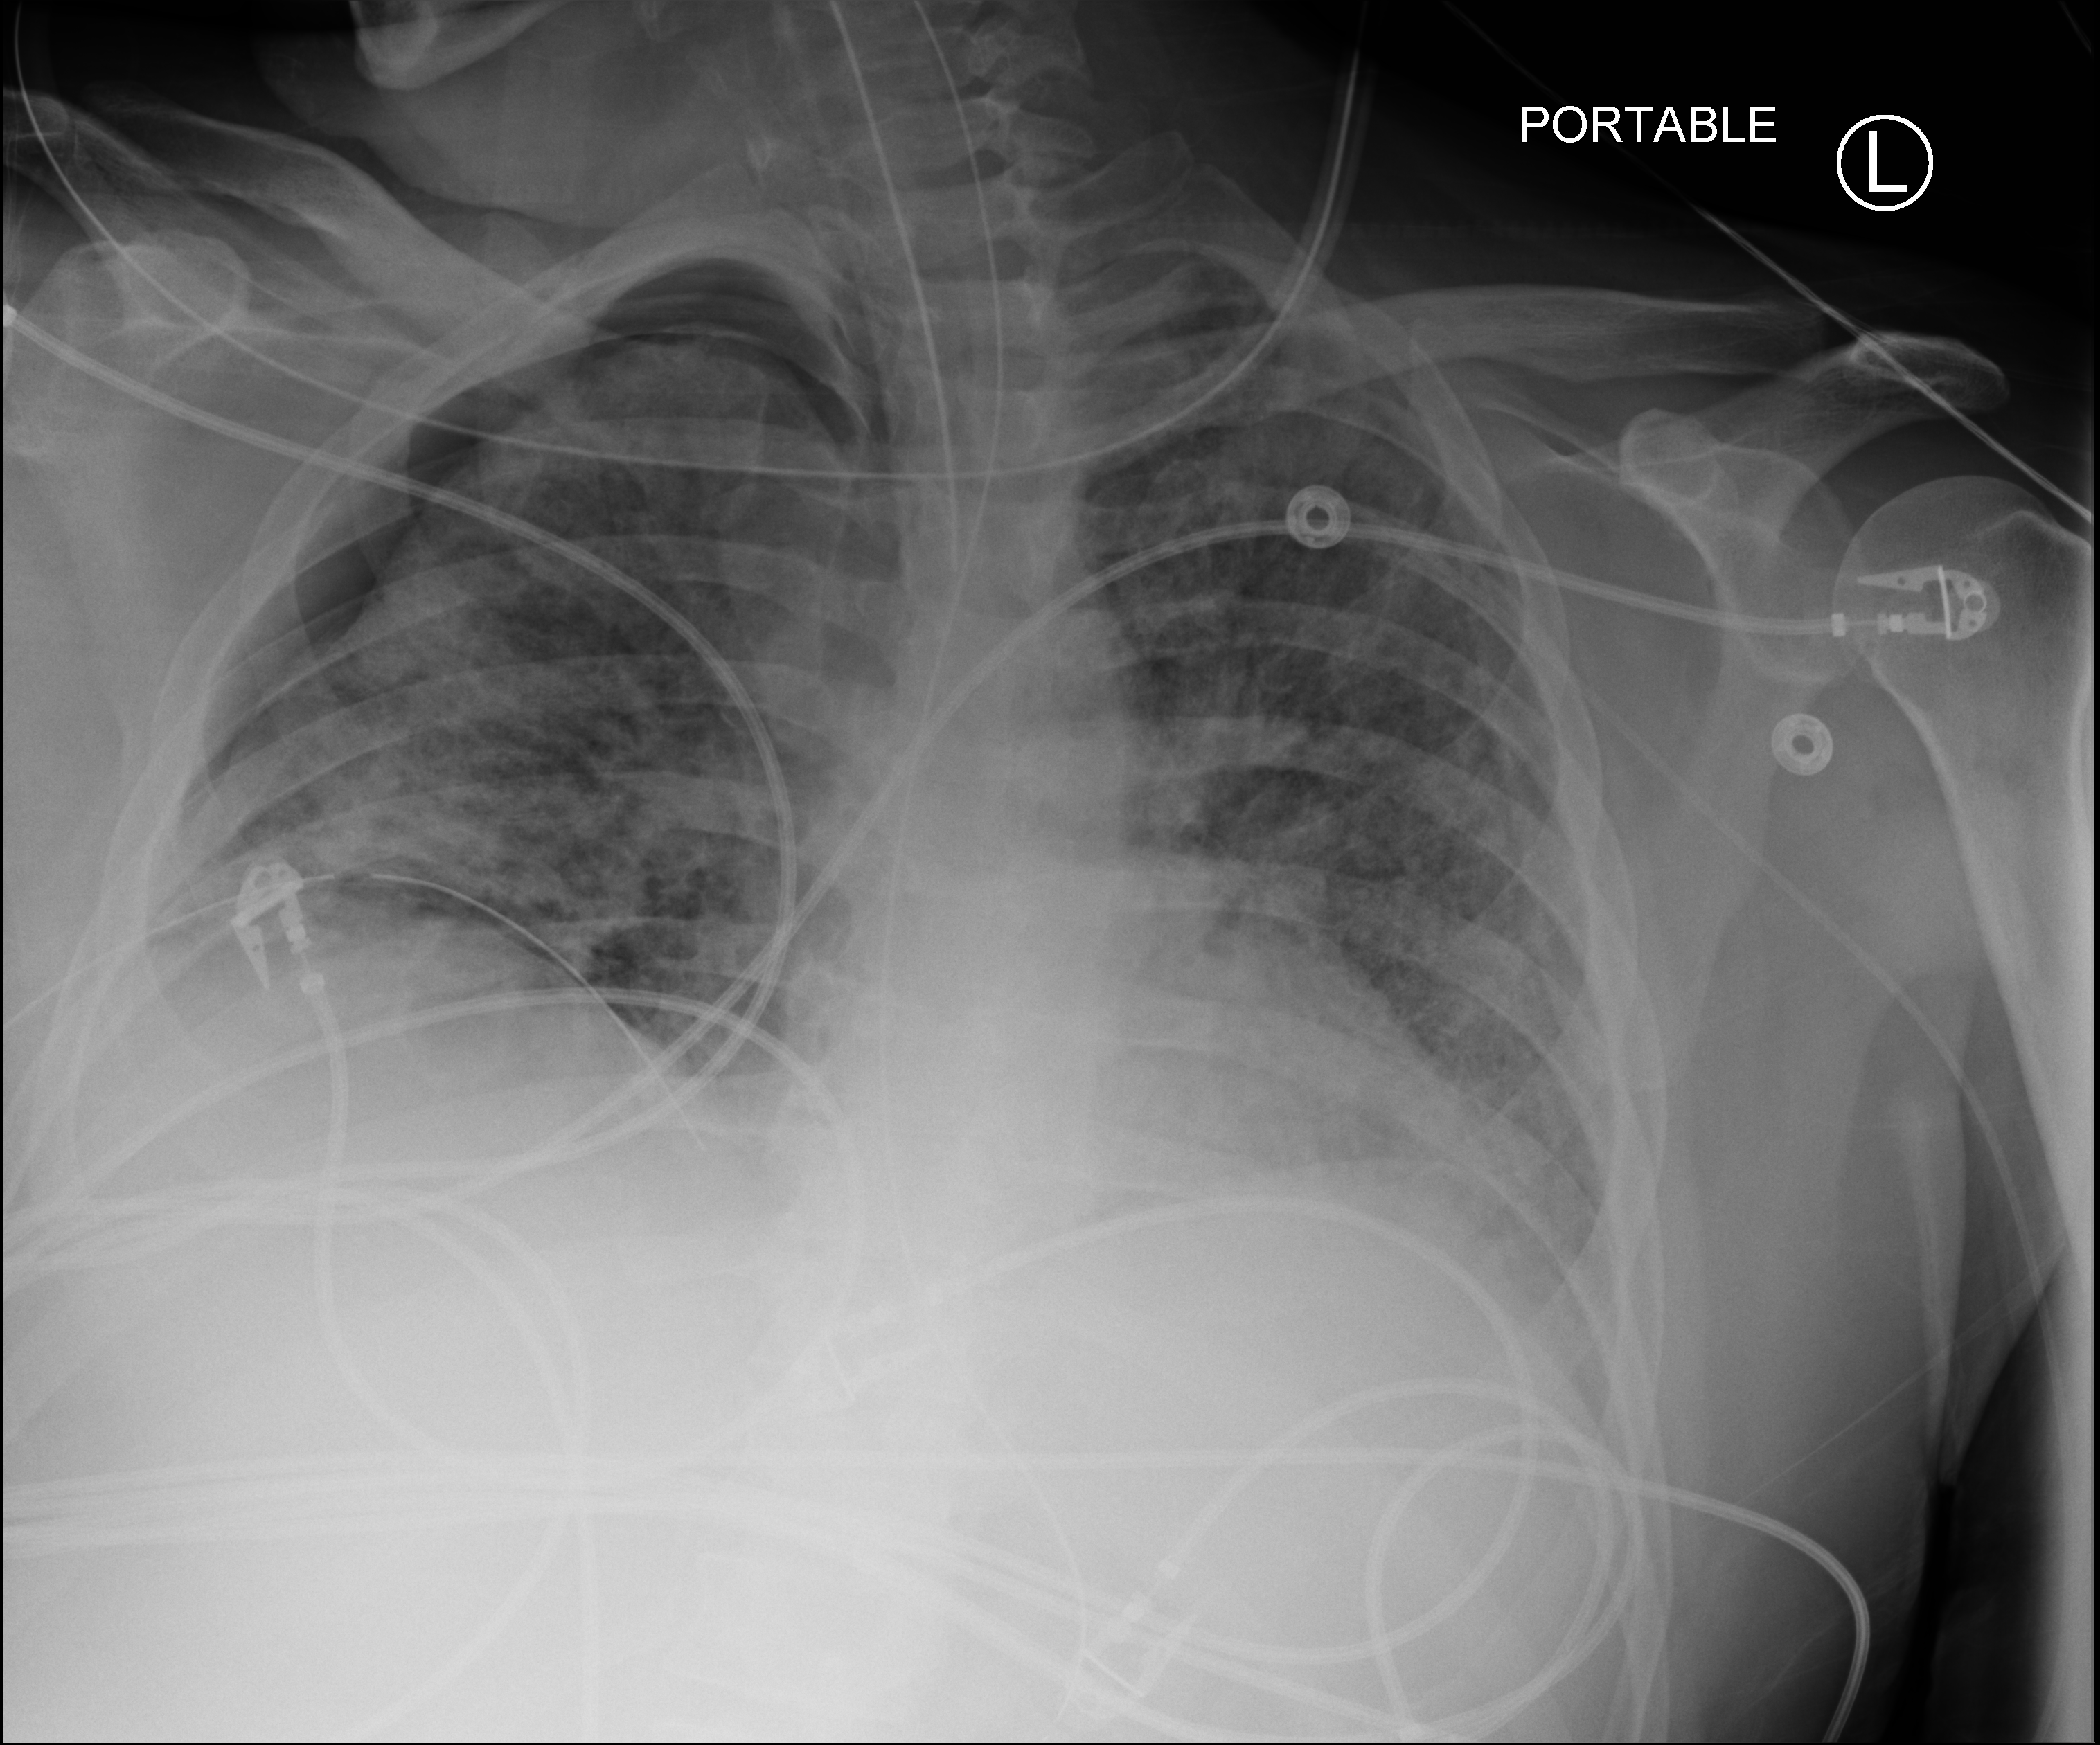
Chest X-ray (portable); anteroposterior (AP) projection. Male patient hospitalised with COVID-19, age 18–59 years.
Admission-level facts for this patient (not findings on this image; timing relative to this image not recorded):
- mechanically ventilated during this hospital stay: yes